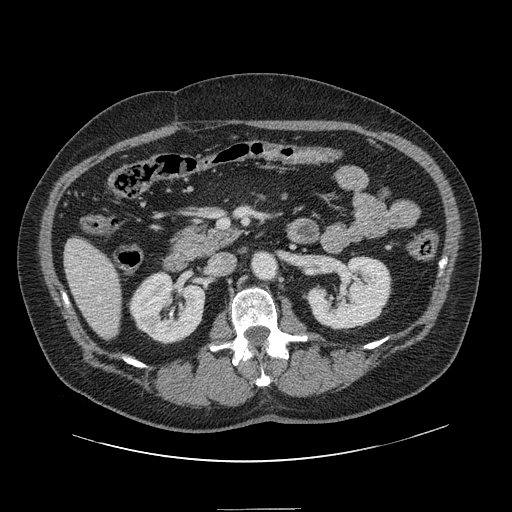
Contrast-enhanced abdominal CT, one axial slice. Position 49 of 154 along the scan axis. 120 kVp. Intravenous contrast given. Soft-tissue window (W 400 / L 40 HU). 2.5 mm slice thickness. 512 × 512 image matrix, field of view 451 × 451 mm. Male patient, age 61 years. Case-level facts recorded for this patient, not image findings: diagnosis: colorectal cancer liver metastases, imaged before liver resection; multiple liver metastases: yes; largest metastasis: 2.6 cm.
Structures marked on this image (expert manual segmentation):
- hepatic veins: bounding box <98,296,101,301> (left, top, right, bottom; pixels)
- liver: <66,239,121,338>
- planned liver remnant (the part of the liver to remain after resection): <66,239,121,339>